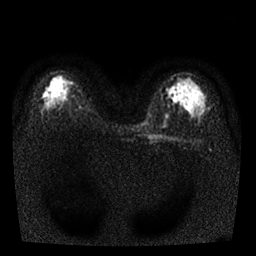
Breast MRI, one axial slice. Slice 16 of 25 in the series (ordered by position). Diffusion-weighted series; image 2 of 4 stored at this slice position (different b-values; order by instance number). 1.5 T. 4 mm slice thickness. 256 × 256 image matrix. Female patient.
Structures marked on this image (outlined manually by an expert reader):
- tumour on diffusion-weighted imaging: box from (x=44, y=93) to (x=50, y=97) px